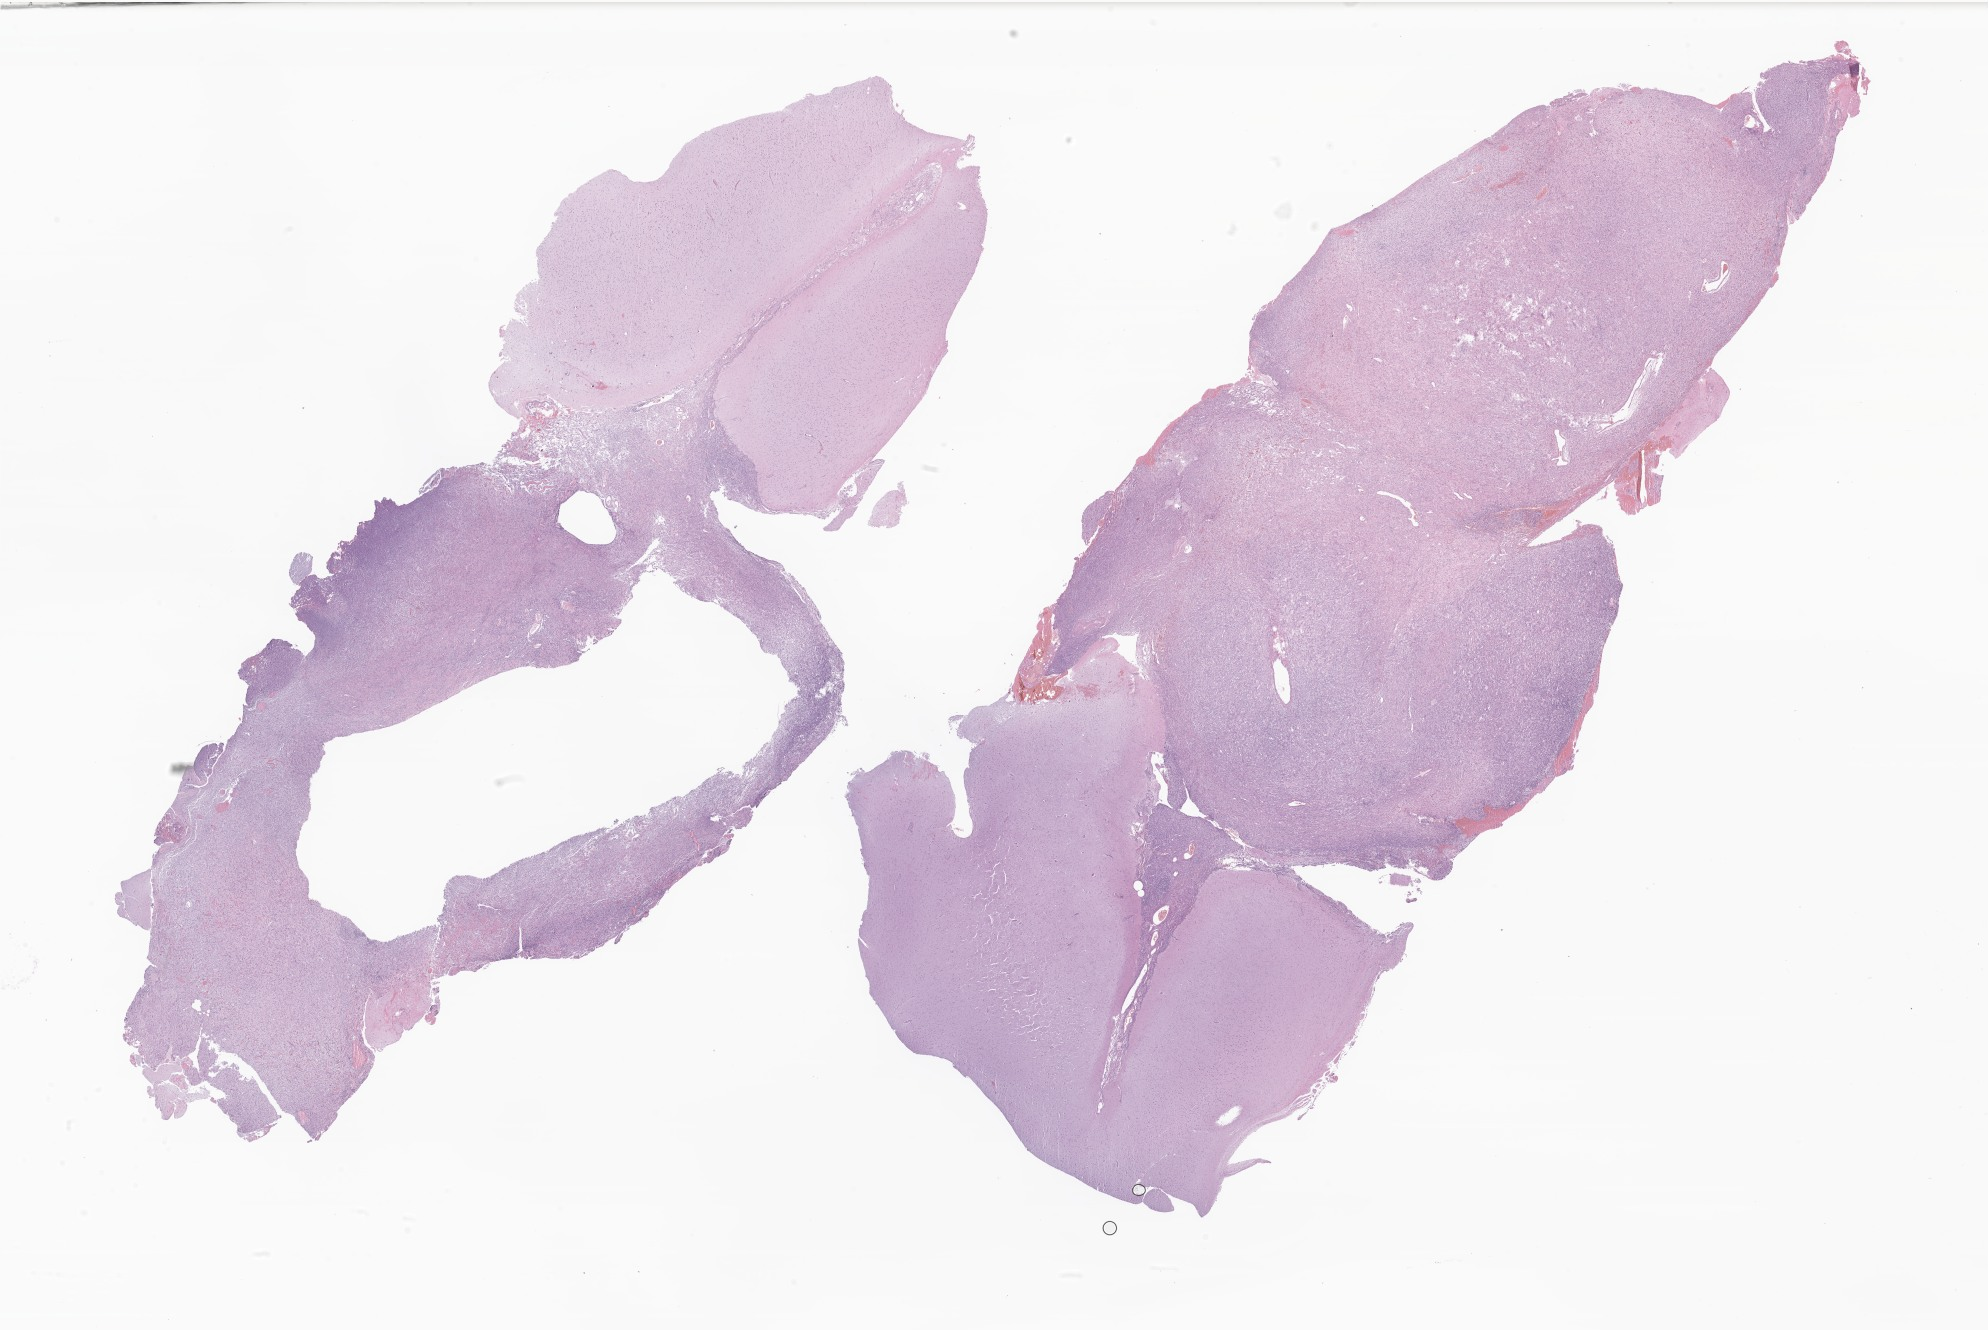
Whole-slide image, haematoxylin and eosin stain of tumor tissue from the brain — whole scanned area (about 33.5 x 22.4 mm) shown as a low-resolution overview; FFPE section. Patient: male, age 929 days (about 2.5 years).
- diagnosis: Ganglioglioma, NOS